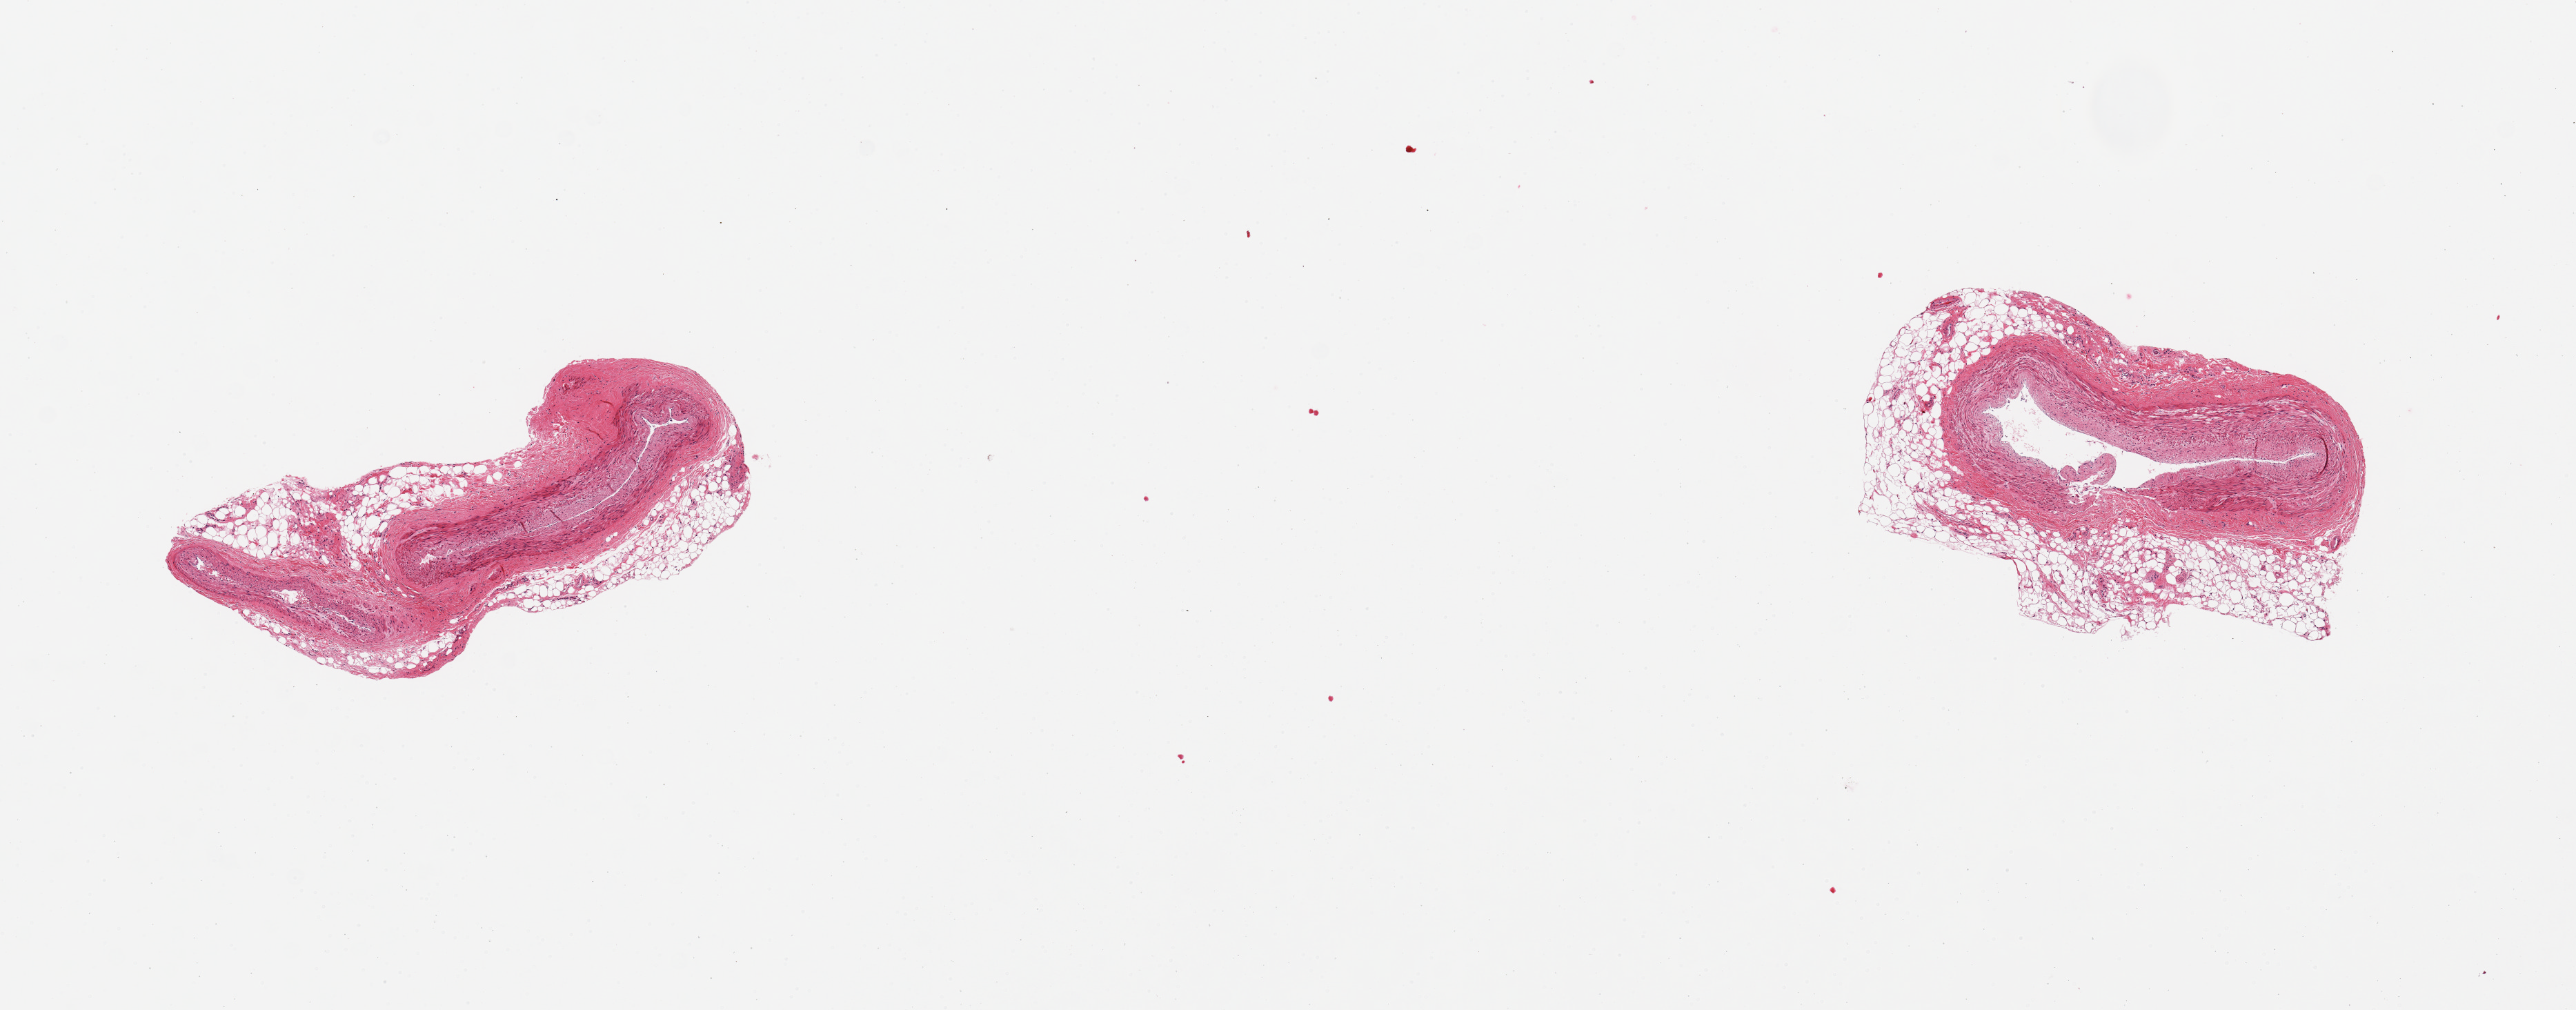
Whole-slide image, hematoxylin and eosin (H&E) stain, brightfield, shown as a low-resolution overview of the whole scanned area (about 14.8 x 5.8 mm, from a 20x scan); PAXgene-fixed paraffin-embedded (PFPE) section; section of coronary artery (target tissue); donor tissue sample. Donor sex: male.
- reviewer comment on this tissue sample: 2 pieces; partial peripheral rim of fat up to 460um and 381um